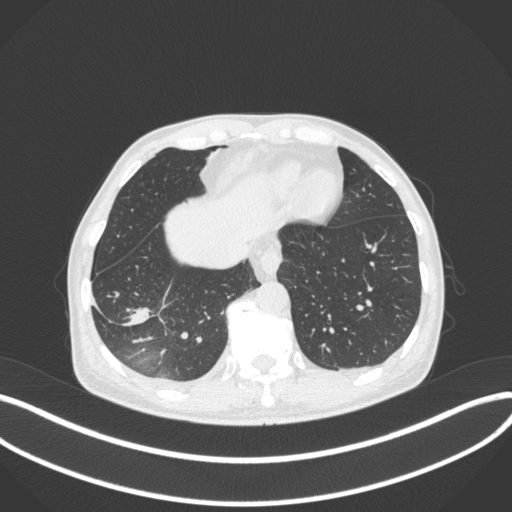
Chest CT, one axial slice; position 88 of 385 along the scan axis; 120 kVp; lung window (W 1500 / L -600 HU); 512 × 512 image matrix, field of view 400 × 400 mm. Patient: male, 64 years. From the clinical record (not read from this slice): clinical TNM (as recorded): T3 N0 M0; histopathological grade: G2-3.
Annotated regions visible in this slice (bounding box drawn by a radiologist):
- lung tumour (recorded histology: adenocarcinoma): bounding box (x1, y1, x2, y2) in pixels: (115, 299, 153, 330)